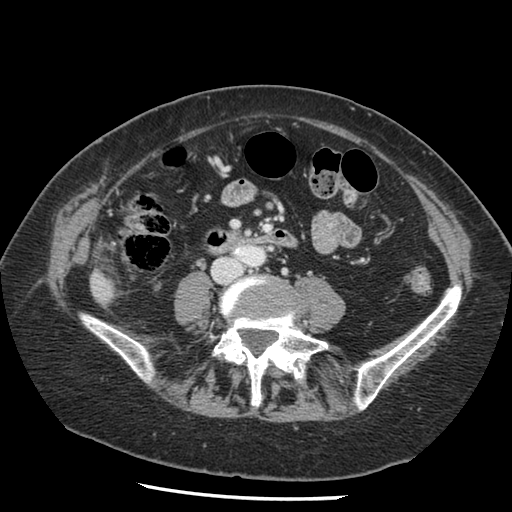
Contrast-enhanced abdominal CT, one axial slice; position 13 of 148 along the scan axis; intravenous contrast given; soft-tissue window (W 400 / L 40 HU); 2.5 mm slice thickness; 512 × 512 image matrix. Female patient, age 85 years. Case-level facts recorded for this patient, not image findings: diagnosis: colorectal cancer liver metastases, imaged before liver resection; multiple liver metastases: no; largest metastasis: 0.9 cm; disease in both lobes: no.
Outlined on this slice (outlined manually by an expert reader):
- liver: bounding box <93,274,113,303> (left, top, right, bottom; pixels)
- planned liver remnant (the part of the liver to remain after resection): <93,274,113,303>